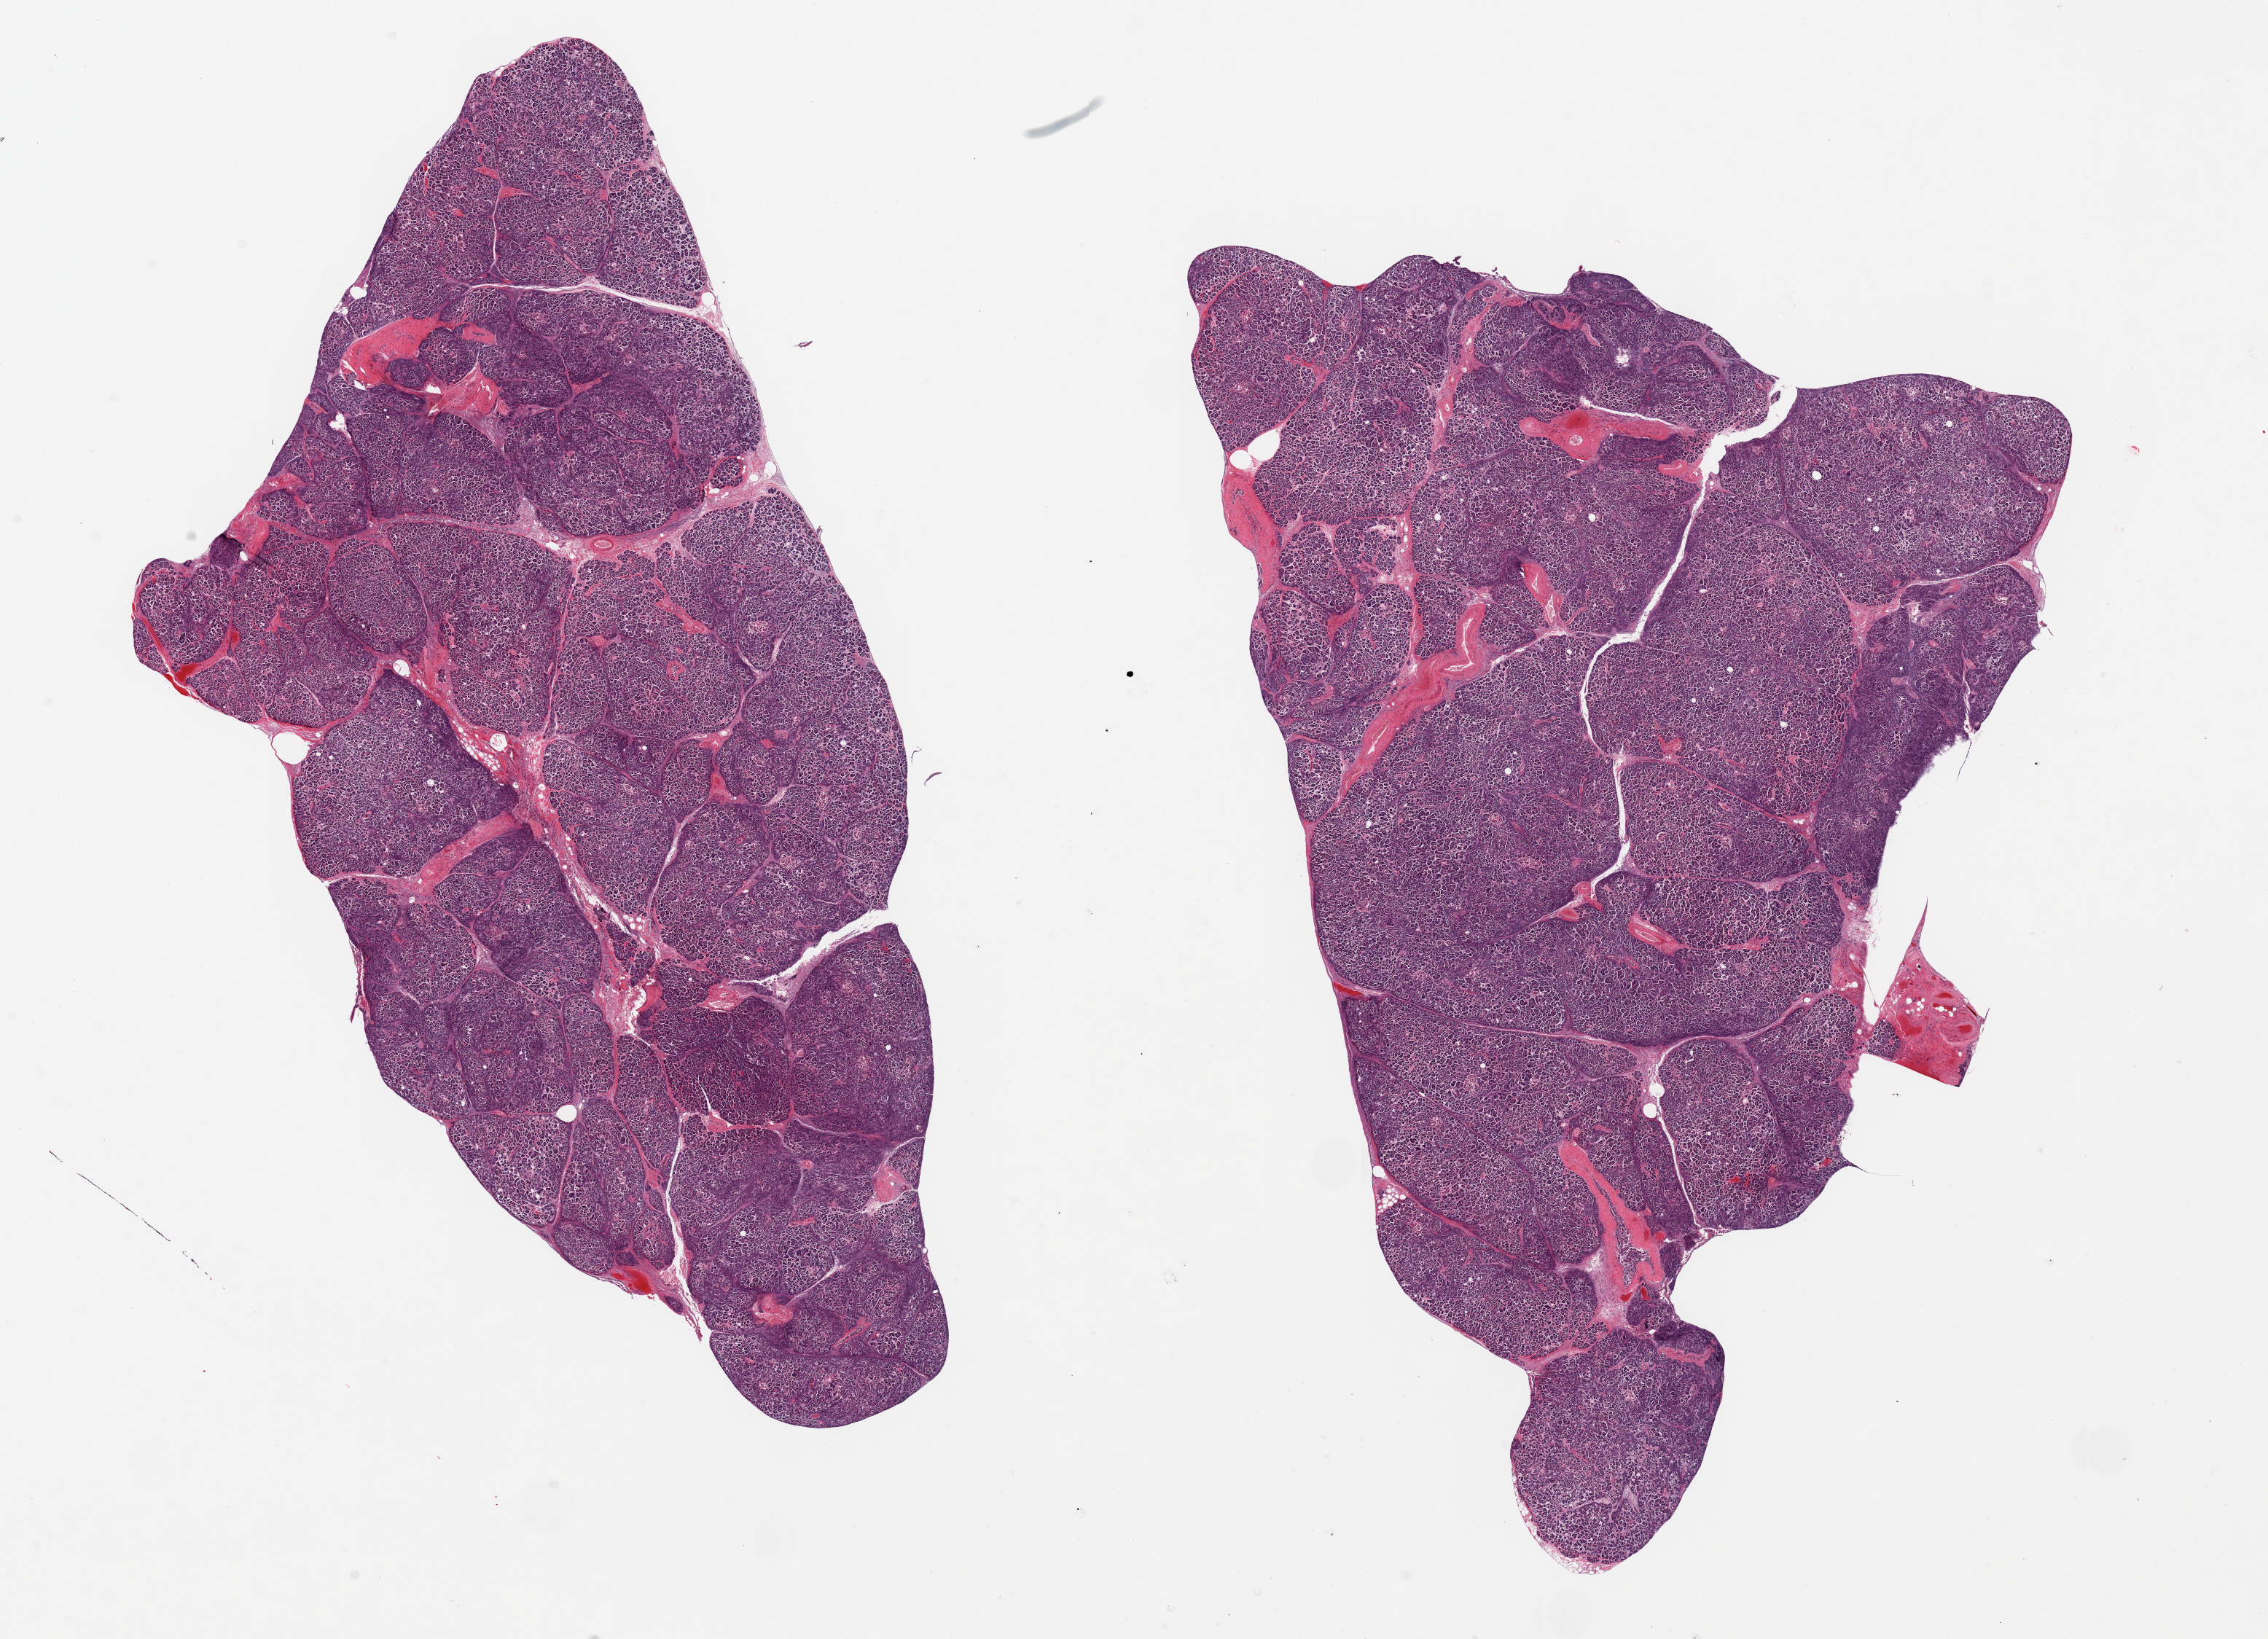
Haematoxylin and eosin whole-slide image — low-resolution overview of the scanned area, about 24.6 x 17.8 mm; PAXgene-fixed paraffin-embedded (PFPE) section; sampled site (target tissue): pancreas; donor tissue sample. Female donor.
Reviewer comment on this tissue sample: 2 pieces; moderate to severe autolysis, sparsely scattered islets.